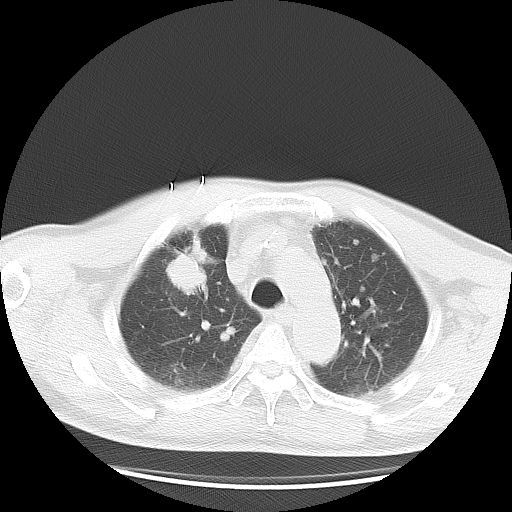
Chest CT, one axial slice; position 23 of 36 along the scan axis; 120 kVp; lung window (W 1500 / L -600 HU); 5 mm slice thickness; 512 × 512 image matrix, field of view 369 × 369 mm. Male patient, age 57 years. Case-level facts recorded for this patient, not image findings: clinical TNM (as recorded): T2 N3 M1a.
Annotated regions visible in this slice (bounding box drawn by a radiologist):
- lung tumour (recorded histology: adenocarcinoma): bounding box (x1, y1, x2, y2) in pixels: (162, 240, 215, 306)